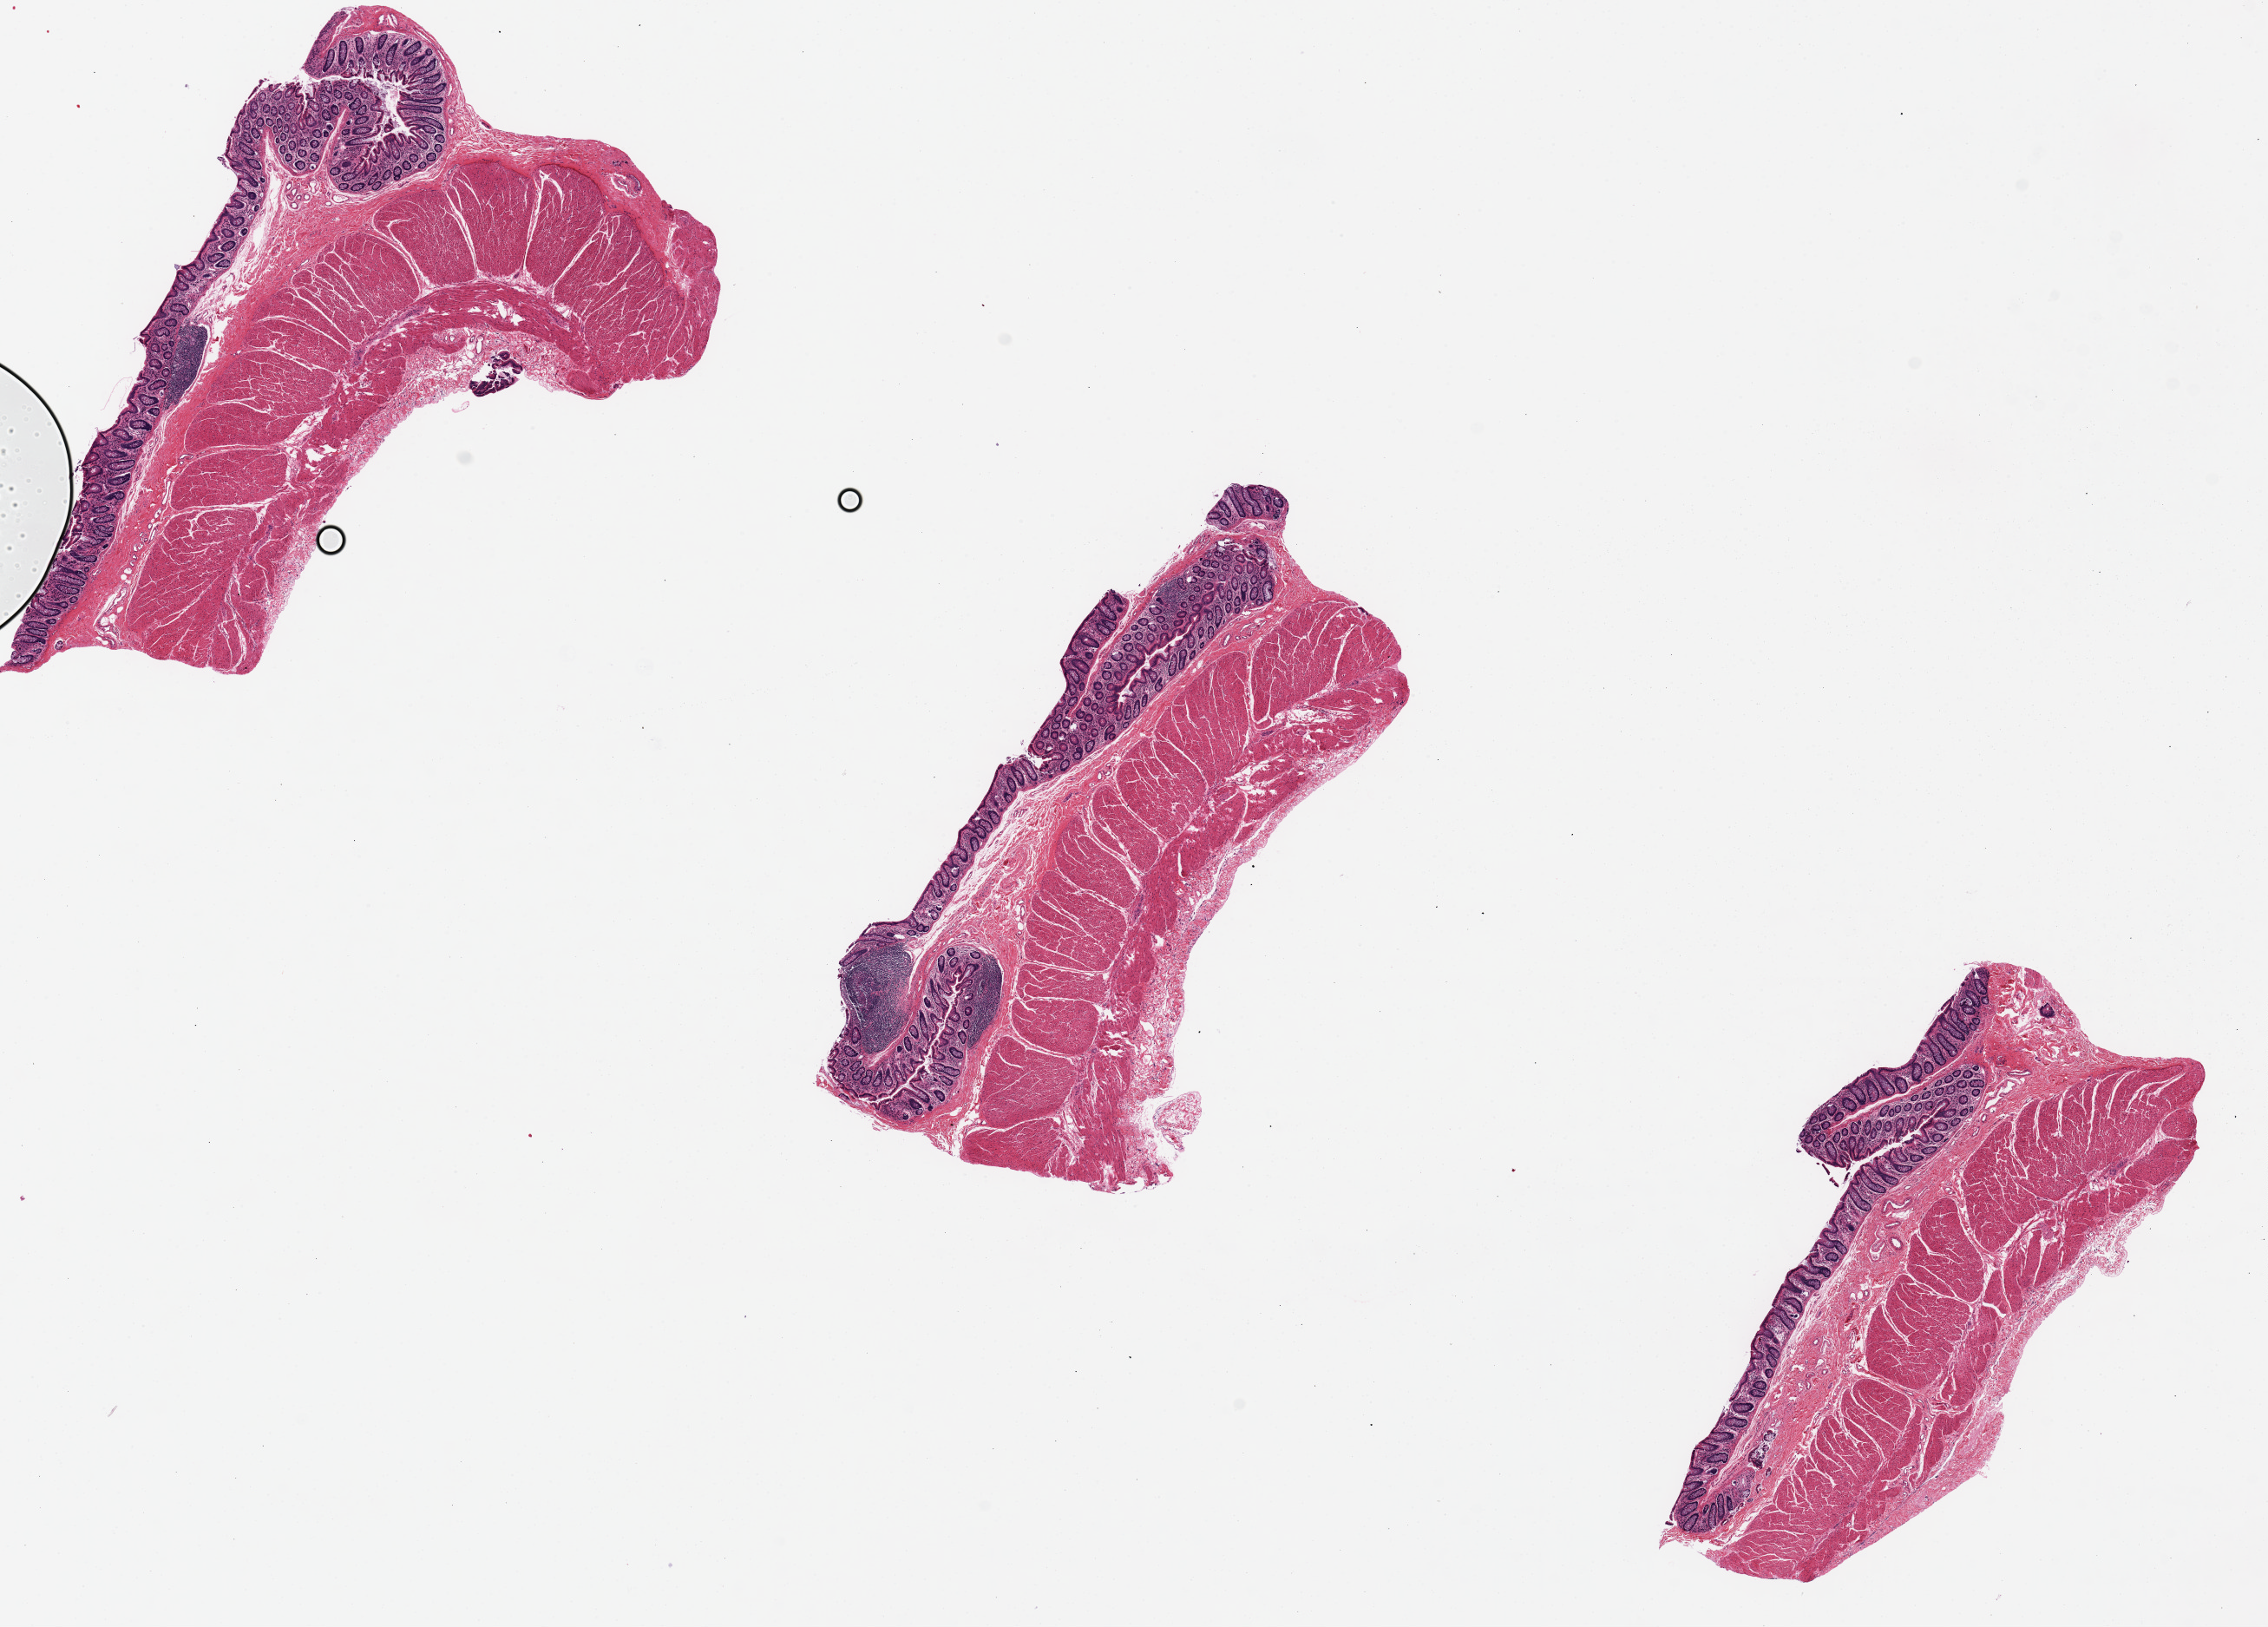
Whole-slide image, hematoxylin and eosin (H&E) stain, brightfield — shown as a low-resolution overview of the whole scanned area (about 20.7 x 14.8 mm); PAXgene-fixed, paraffin-embedded tissue; section of transverse colon (target tissue); donor tissue sample. Donor sex: male.
• review note (as recorded): Mucosa remarkably well preserved and is ~10% of total specimen thickness